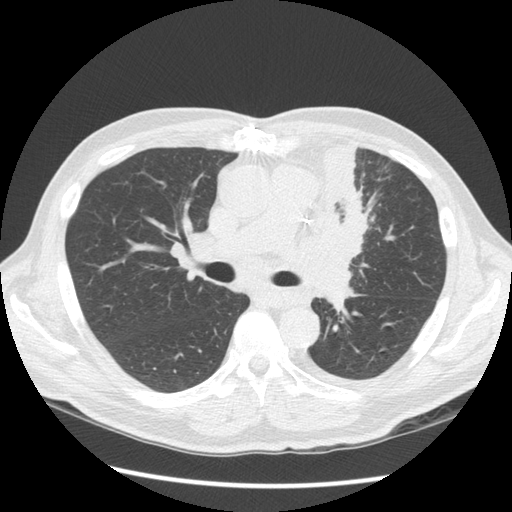
Low-dose screening chest CT, one axial slice; slice 86 of 136 in the series (ordered by position); reconstruction kernel STANDARD; 120 kVp; lung window (W 1500 / L -600 HU); 2.5 mm slice thickness; 512 × 512 image matrix.
Outlined on this slice (expert manual segmentation):
- lesion 1 (tumor, upper lobe of left lung): bounding box (x1, y1, x2, y2) in pixels: (307, 146, 366, 311)